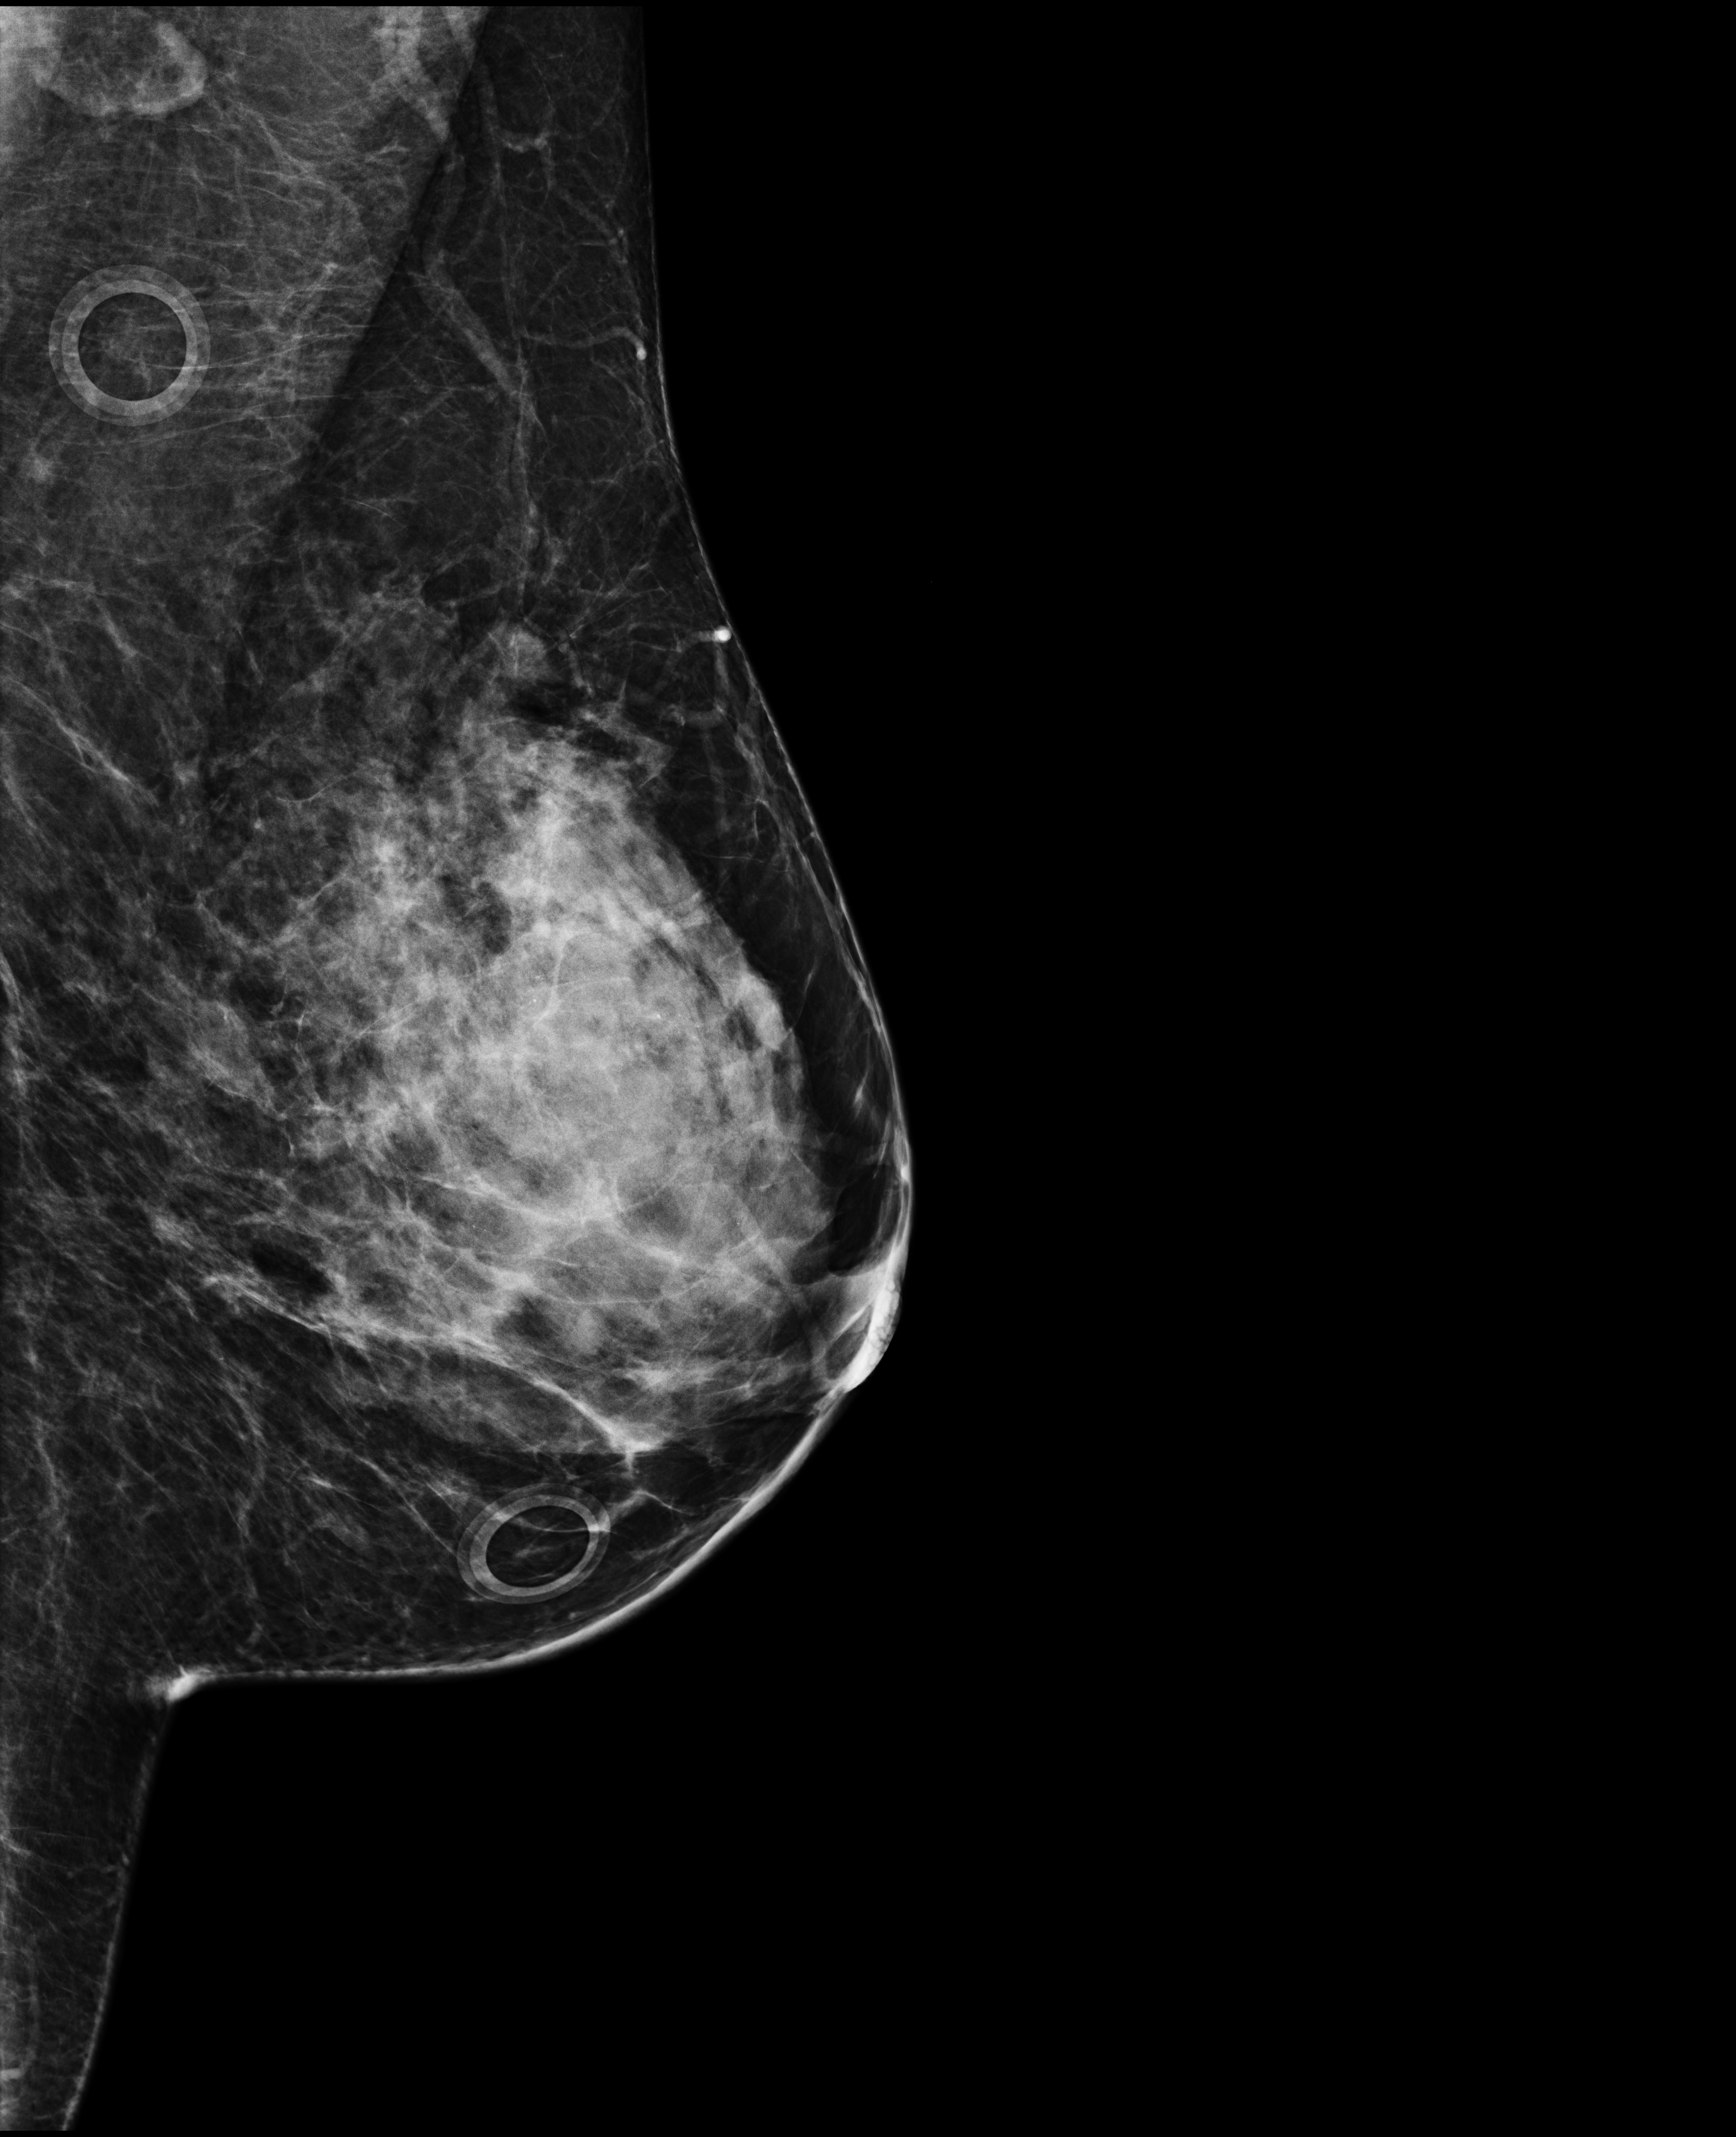
Annual screening mammography examination; compressed breast thickness 60 mm. Patient: female, 46 years.
Image type: full-field digital mammogram. Breast: left. Projection: mediolateral oblique (MLO) view.